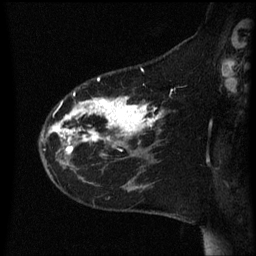
Breast MRI (dynamic contrast-enhanced), one sagittal slice. Slice 17 of 60 in the series (ordered by position). Dynamic contrast-enhanced series, image 2 of 3 at this slice position (ordered by acquisition). 1.5 T. TE 4.2 ms, TR 8.4 ms. 256 × 256 image matrix. Patient: female, 35 years. Case-level facts recorded for this patient, not image findings: setting: breast cancer imaged before/during neoadjuvant chemotherapy; receptor status: HER2-positive.
Outlined on this slice (semi-automatic segmentation, software-assisted and operator-edited):
- analysis volume of interest (the breast-tissue region the enhancement analysis was run in; not a lesion): bounding box [x1, y1, x2, y2] px = [40, 78, 167, 163]
- tumour enhancement mask (voxels above the 70 % enhancement threshold inside the analysis volume of interest): [49, 98, 164, 155]